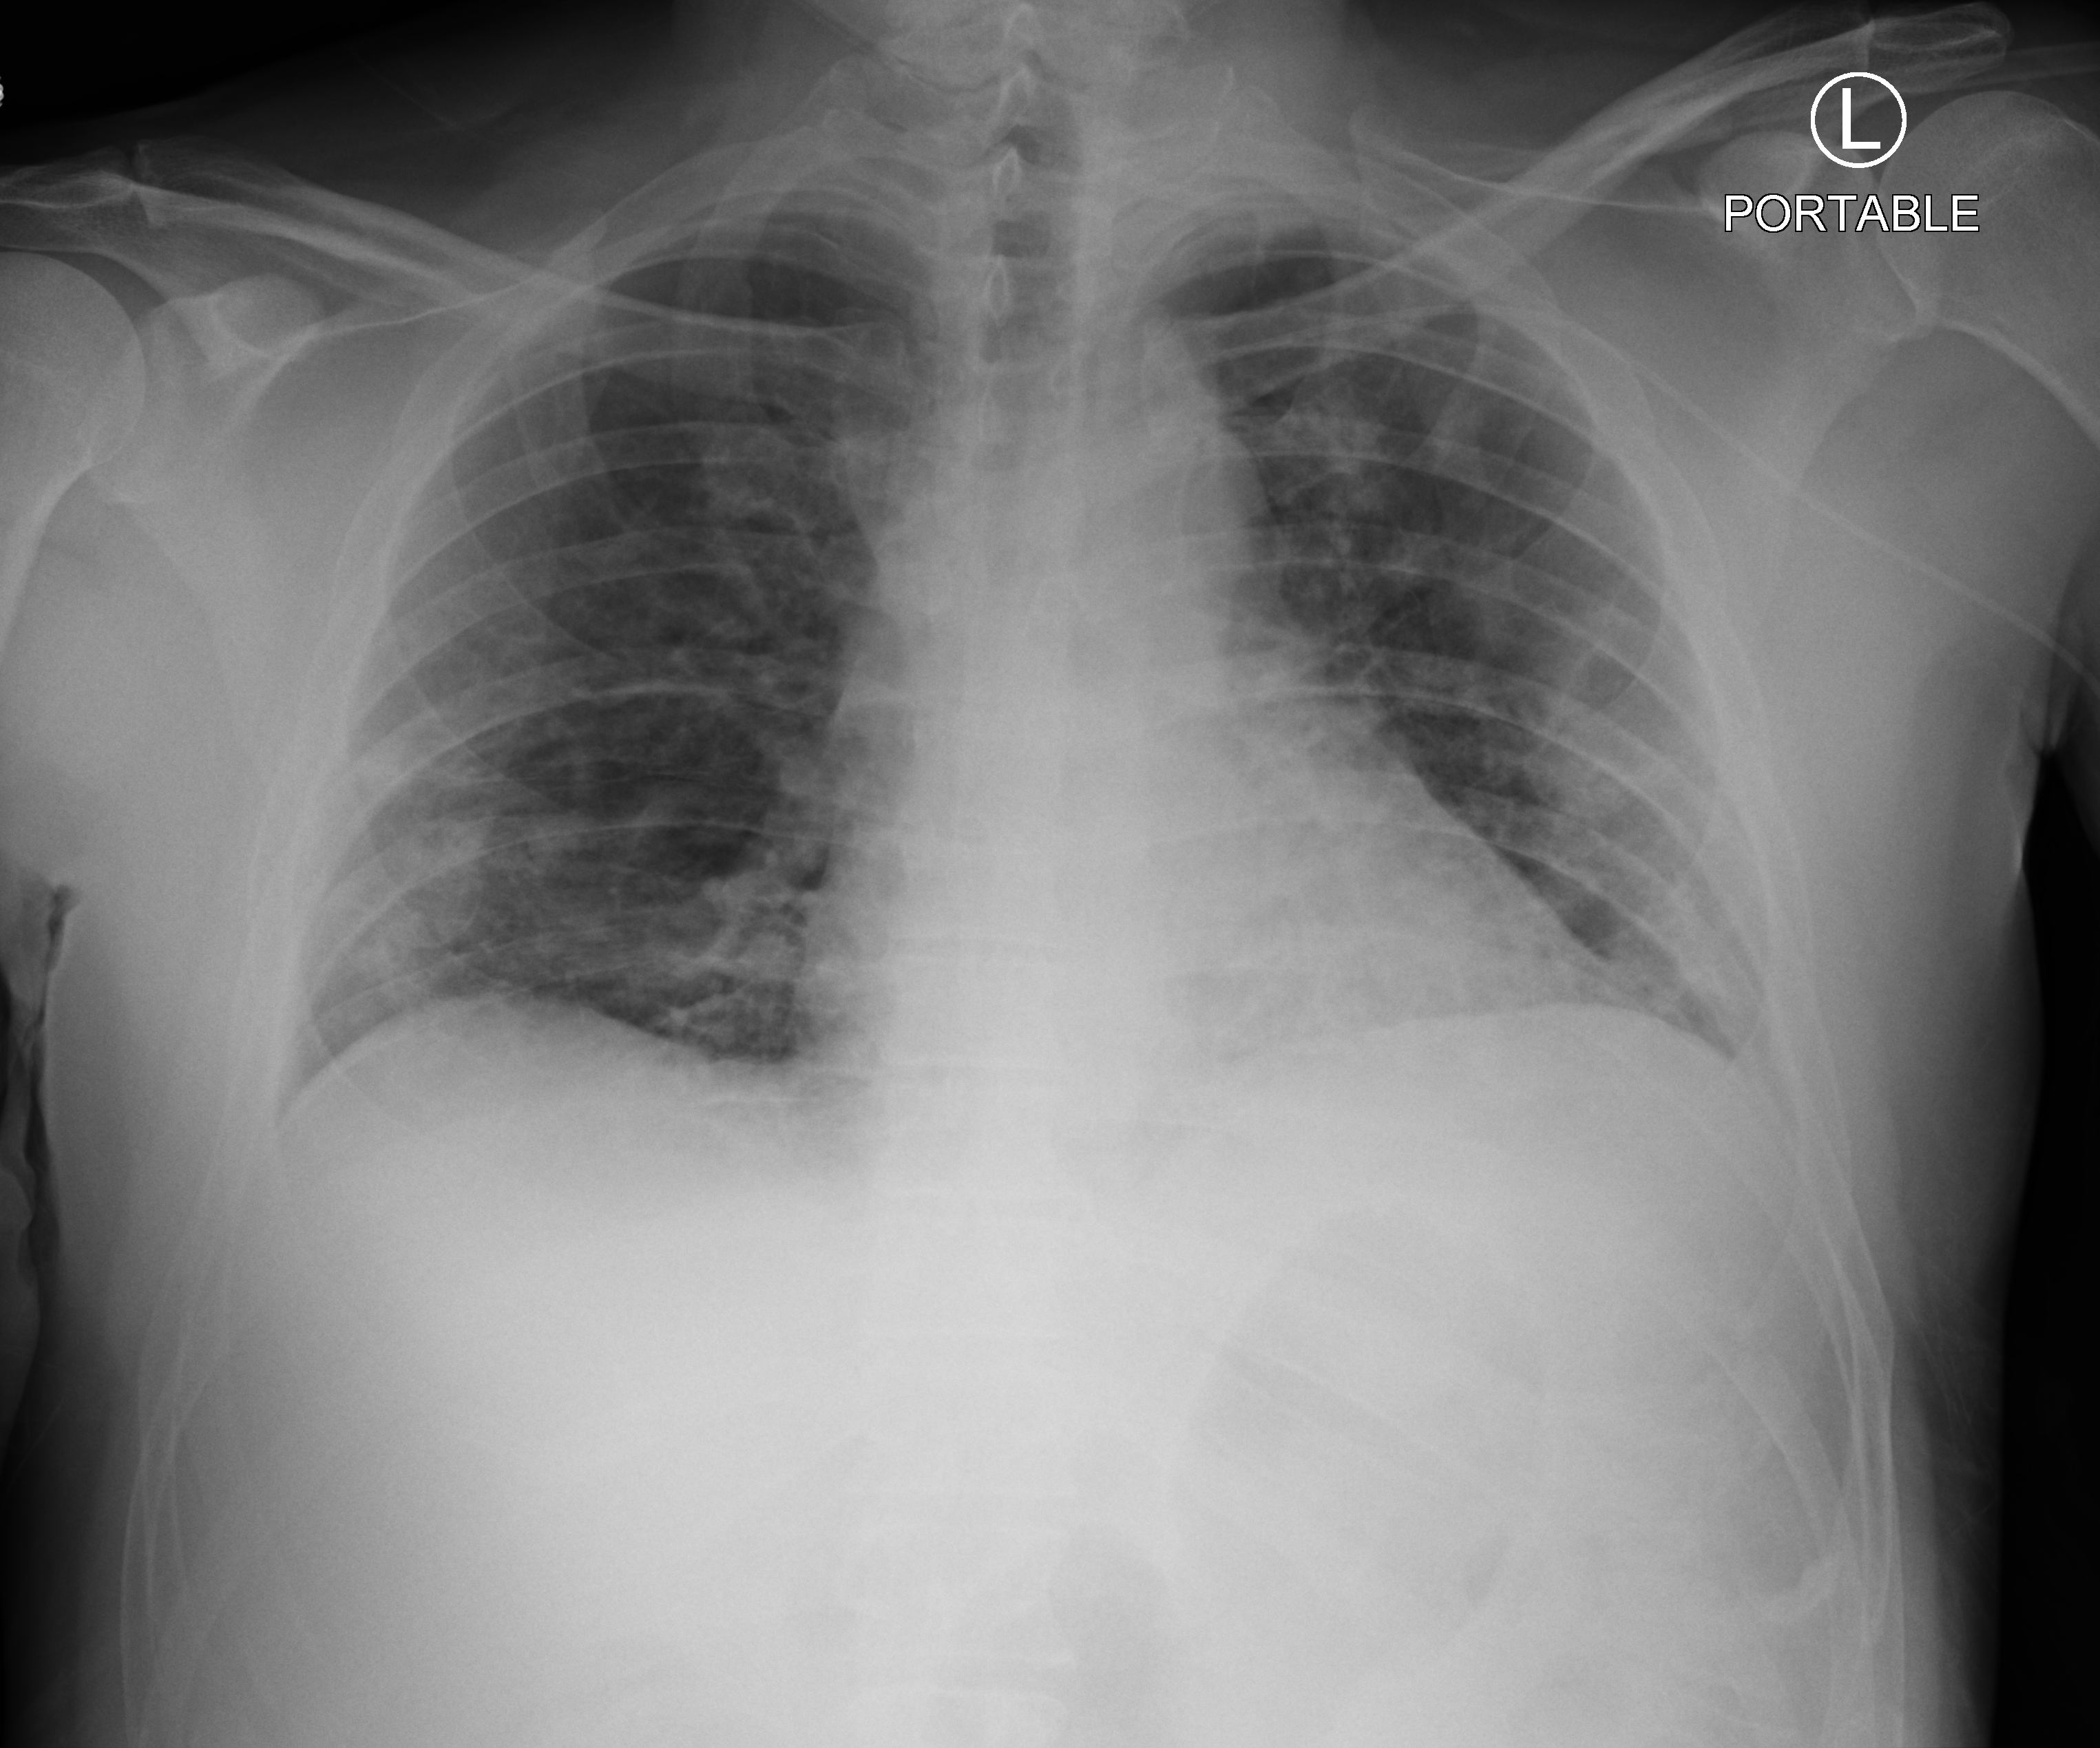
Chest X-ray (portable), anteroposterior (AP) projection. Male patient hospitalised with COVID-19, age 18–59 years.
Hospital-stay facts (about this admission, not read from this image; timing relative to this image not recorded): admitted to intensive care during this hospital stay: yes; mechanically ventilated during this hospital stay: no.